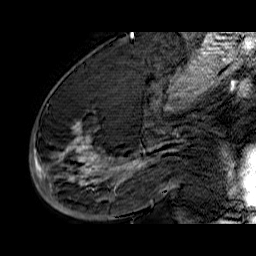
Breast MRI (dynamic contrast-enhanced), one sagittal slice. Slice 35 of 60 in the series (ordered by position). Dynamic contrast-enhanced series, time point 2 of 6 at this slice position (early post-contrast). 1.5 T. TE 6.5 ms, TR 32.9 ms. 4 mm slice thickness. 256 × 256 image matrix, field of view 200 × 200 mm. Female patient. Case-level facts recorded for this patient, not image findings: setting: breast cancer imaged before/during neoadjuvant chemotherapy; receptor status: HR-positive, HER2-negative.
Annotated regions visible in this slice (semi-automatic segmentation, software-assisted and operator-edited):
- analysis volume of interest (the breast-tissue region the enhancement analysis was run in; not a lesion): bounding box <33,74,176,210> (left, top, right, bottom; pixels)
- tumour enhancement mask (voxels above the 100 % enhancement threshold inside the analysis volume of interest): <33,134,173,190>